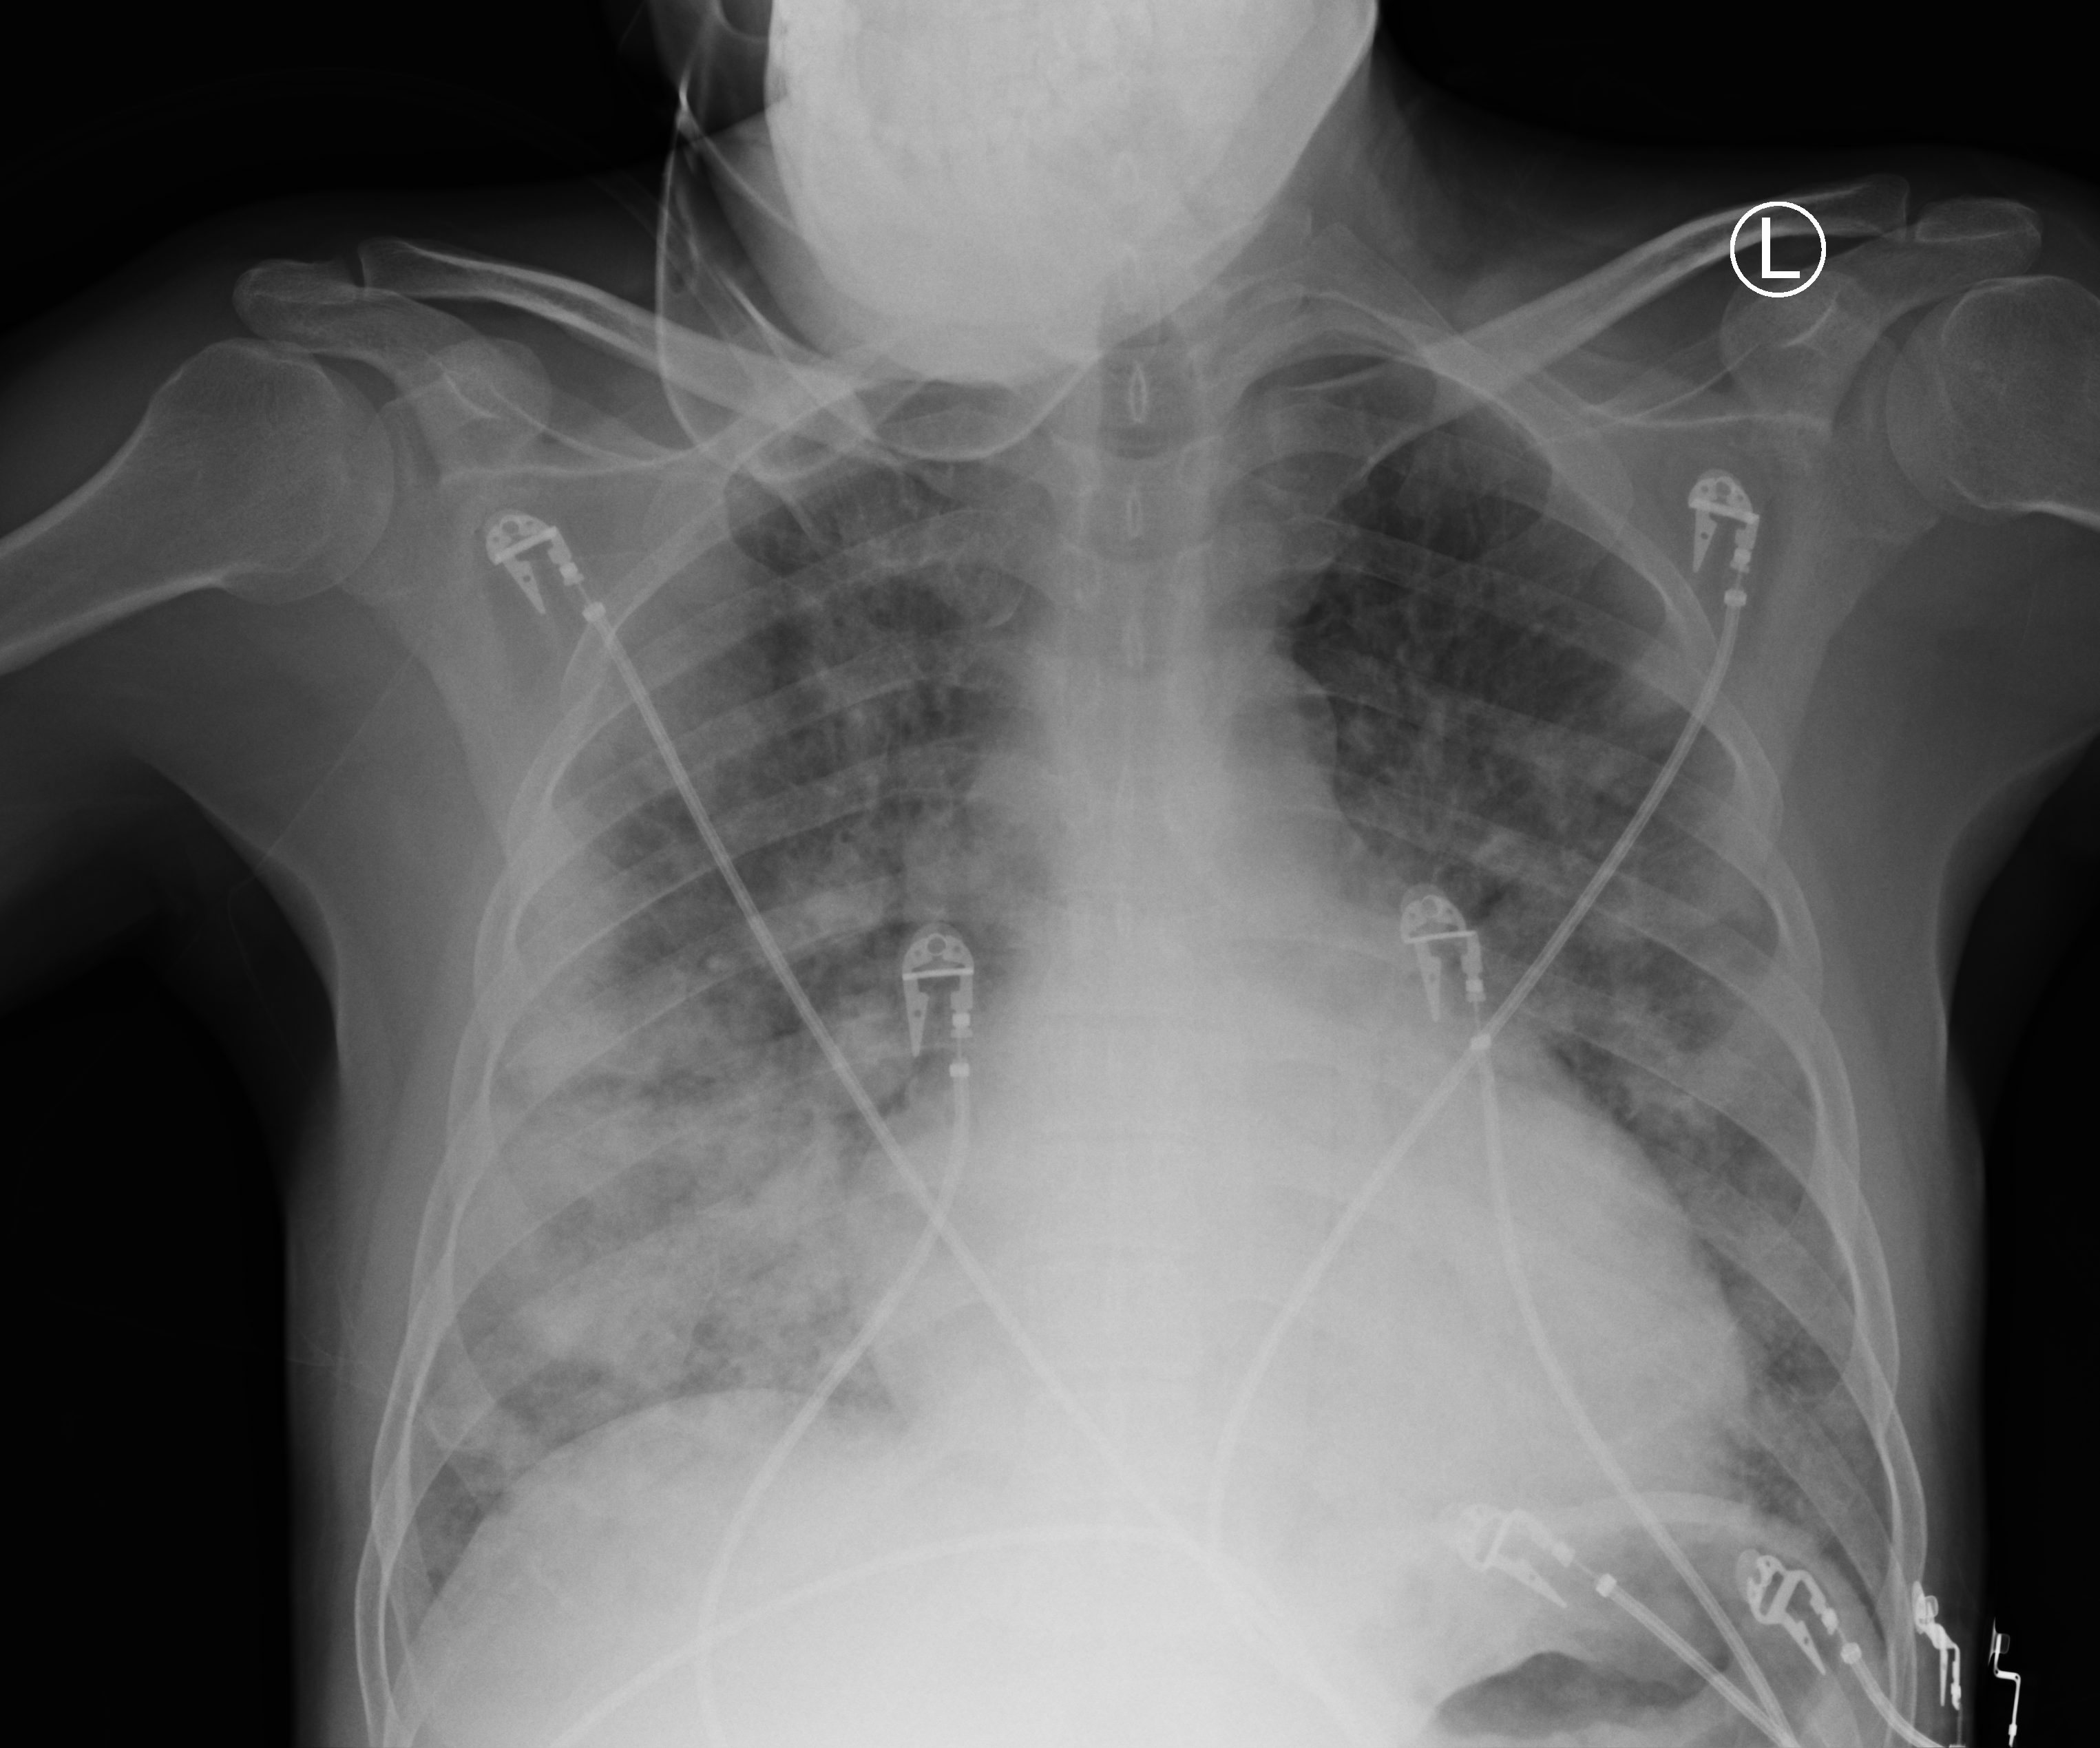
Portable chest radiograph, anteroposterior (AP) projection. Patient hospitalised with COVID-19; male, aged 18–59 years.
From the hospital-stay record, not from the radiograph (when in the stay this image was taken is not recorded): mechanically ventilated during this hospital stay: no.